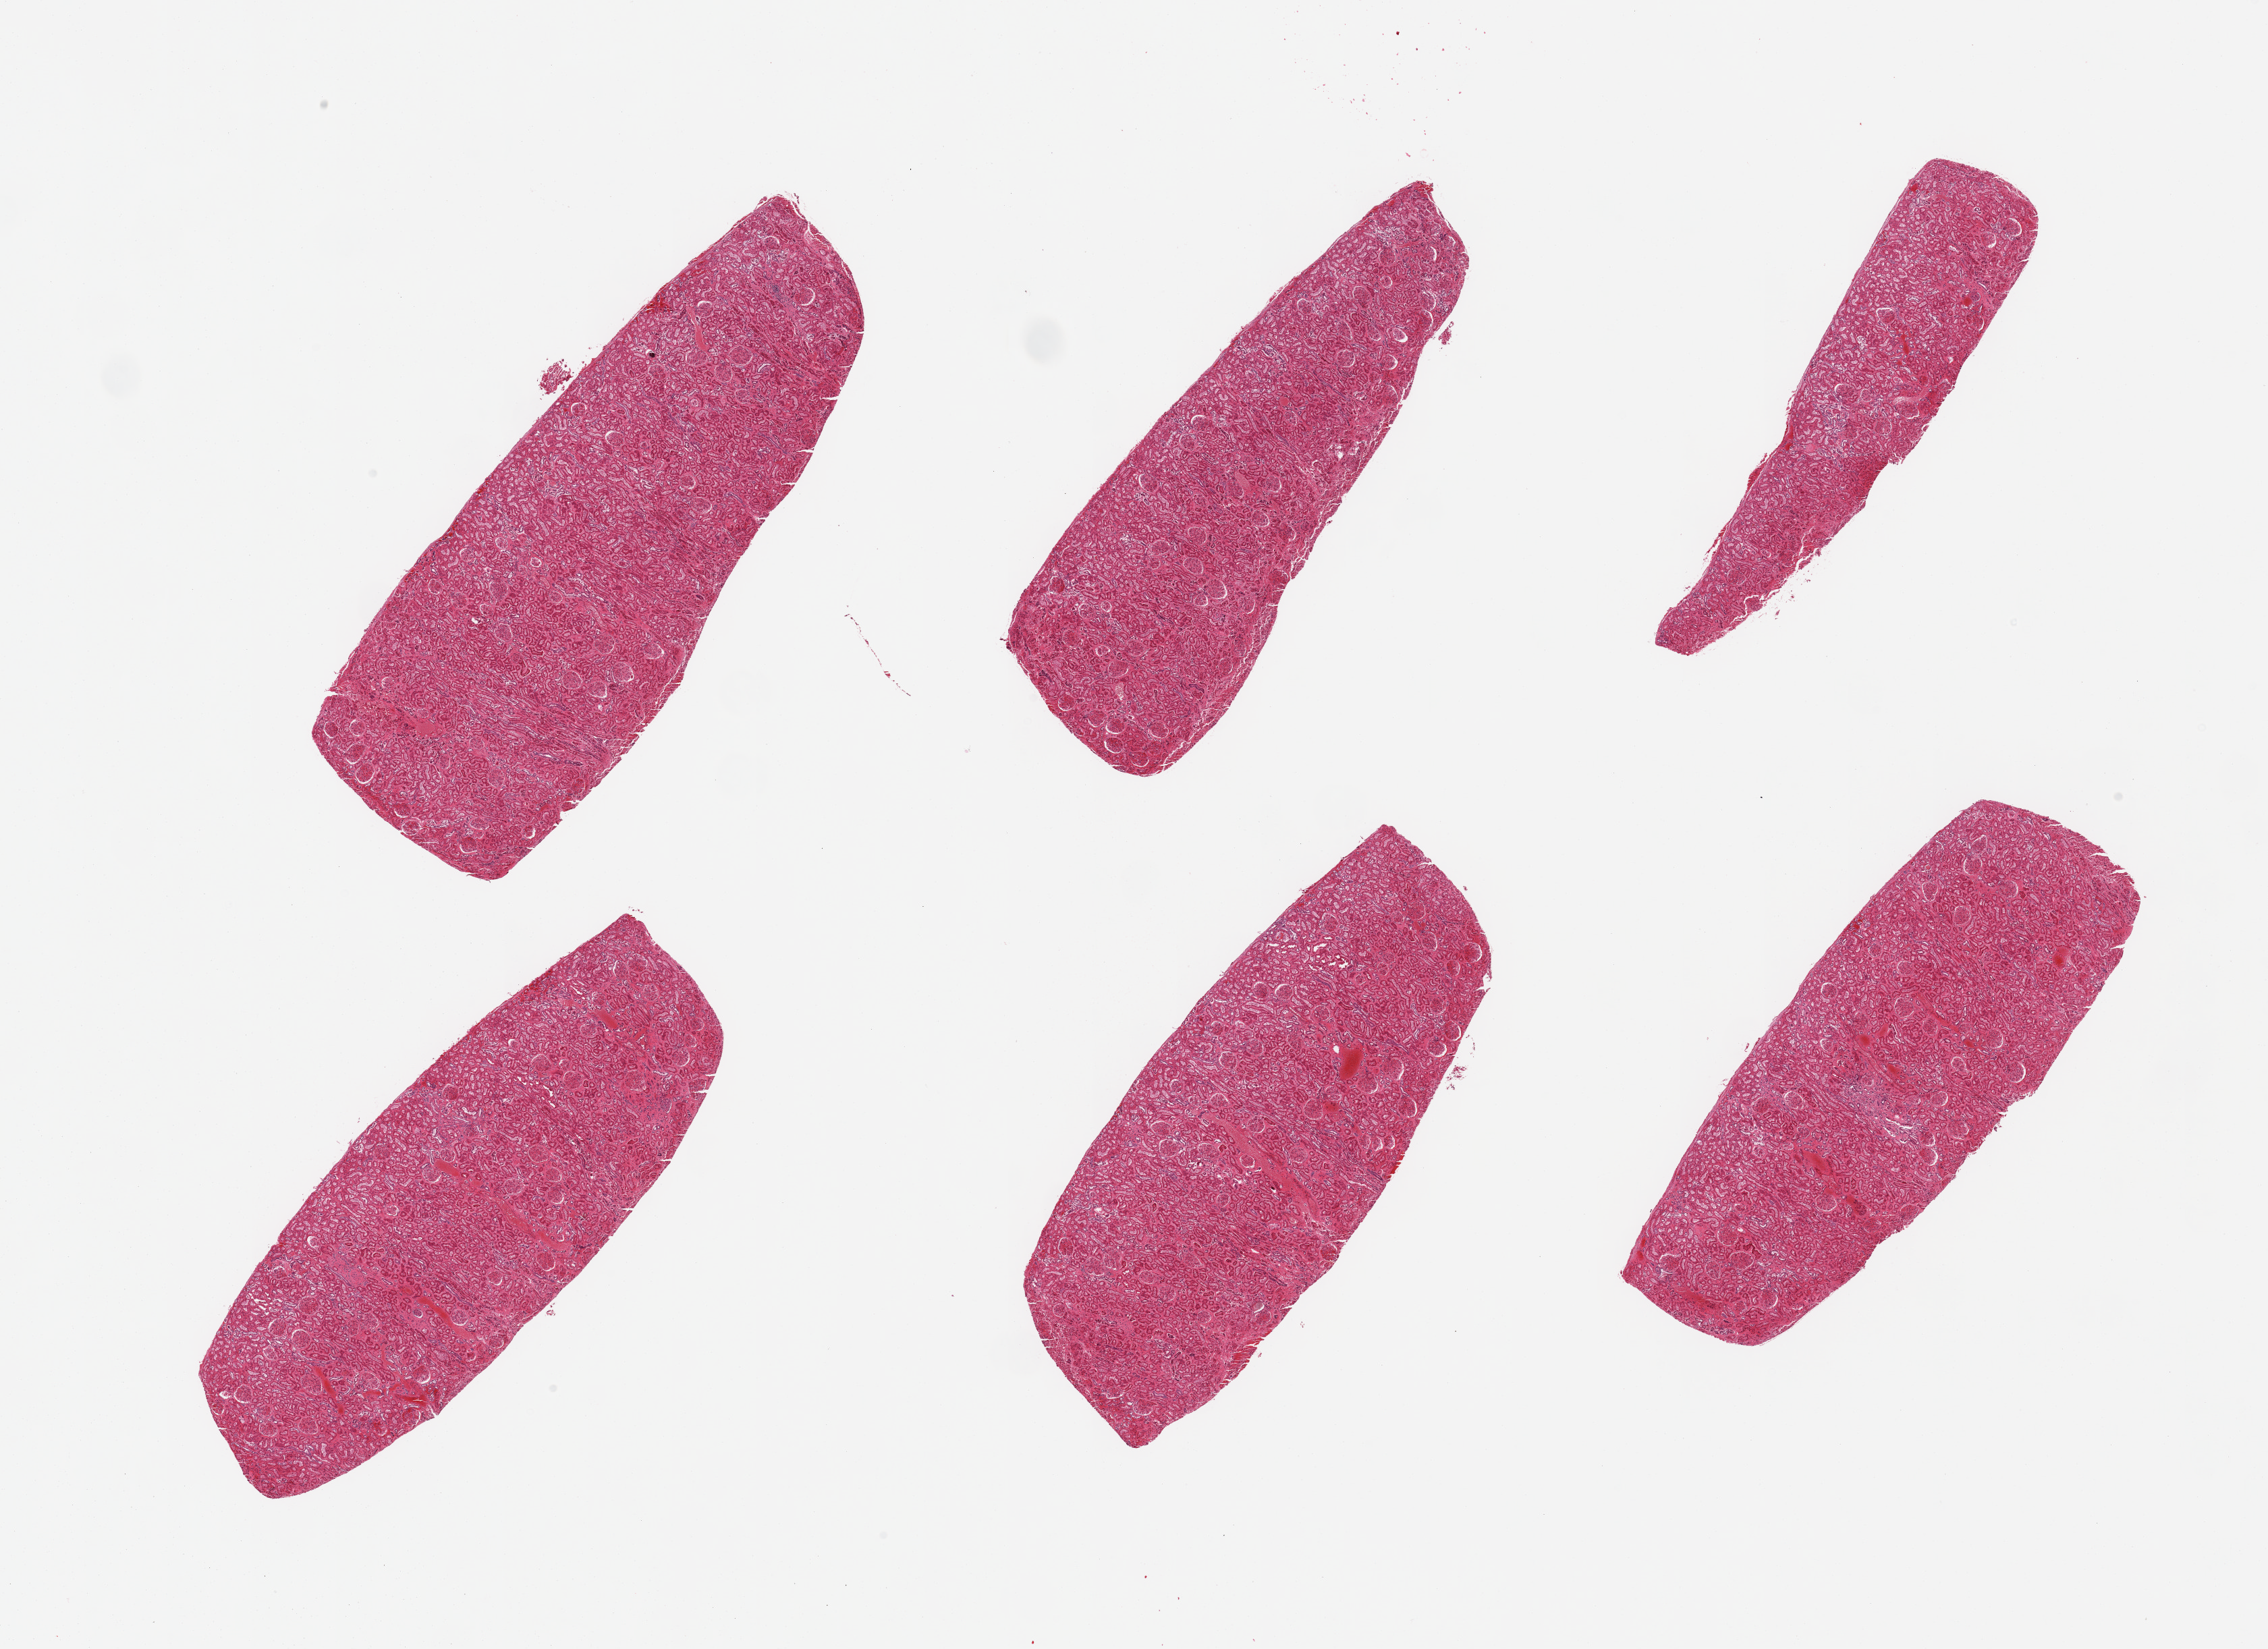
Hematoxylin and eosin (H&E) whole-slide image, shown as a low-resolution overview of the whole scanned area (about 26.6 x 19.3 mm); PAXgene-fixed paraffin-embedded (PFPE) section; sampled site (target tissue): renal cortex; donor tissue sample. Donor sex: female.
Review note (as recorded): 6 pieces; modrate congestion; no chronic or active lesions.